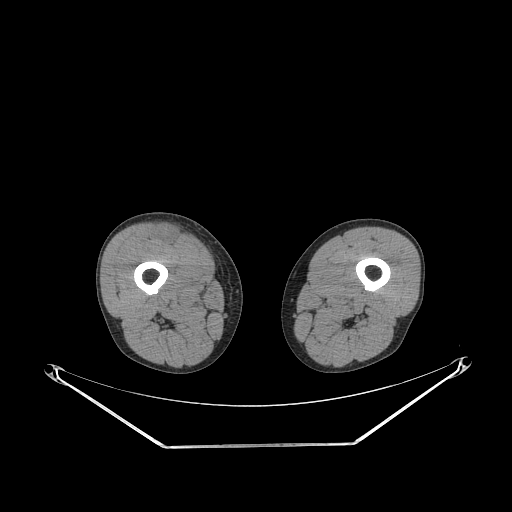
CT of an extremity soft-tissue mass (from a PET/CT study), one axial slice. Reconstruction kernel STANDARD. 140 kVp. Soft-tissue window (W 400 / L 40 HU). 3.75 mm slice thickness. 512 × 512 image matrix, field of view 500 × 500 mm. Male patient. From the clinical record (not read from this slice): histological type: pleiomorphic leiomyosarcoma; grade: intermediate; site of the primary tumour: right thigh.
Annotated regions visible in this slice (expert contour drawn on MRI and transferred to this co-registered scan by the dataset authors):
- gross tumour volume including surrounding oedema: bounding box [x1, y1, x2, y2] px = [157, 226, 182, 243]